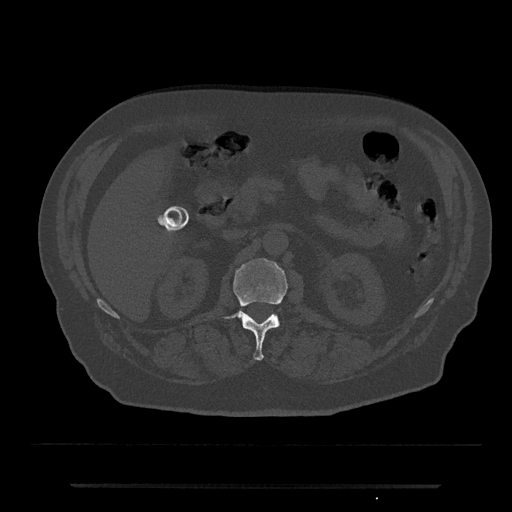
CT including the spine, one axial slice; 120 kVp; bone window (W 1800 / L 400 HU); 0.5 mm slice thickness; 512 × 512 image matrix. Male patient, age 80 years. Case-level facts recorded for this patient, not image findings: primary cancer: prostate; vertebrae with lytic lesions (as recorded): L1, T11.
Outlined on this slice (semi-automatically segmented with operator editing):
- L1 vertebra: bounding box (x1, y1, x2, y2) in pixels: (233, 258, 289, 361)